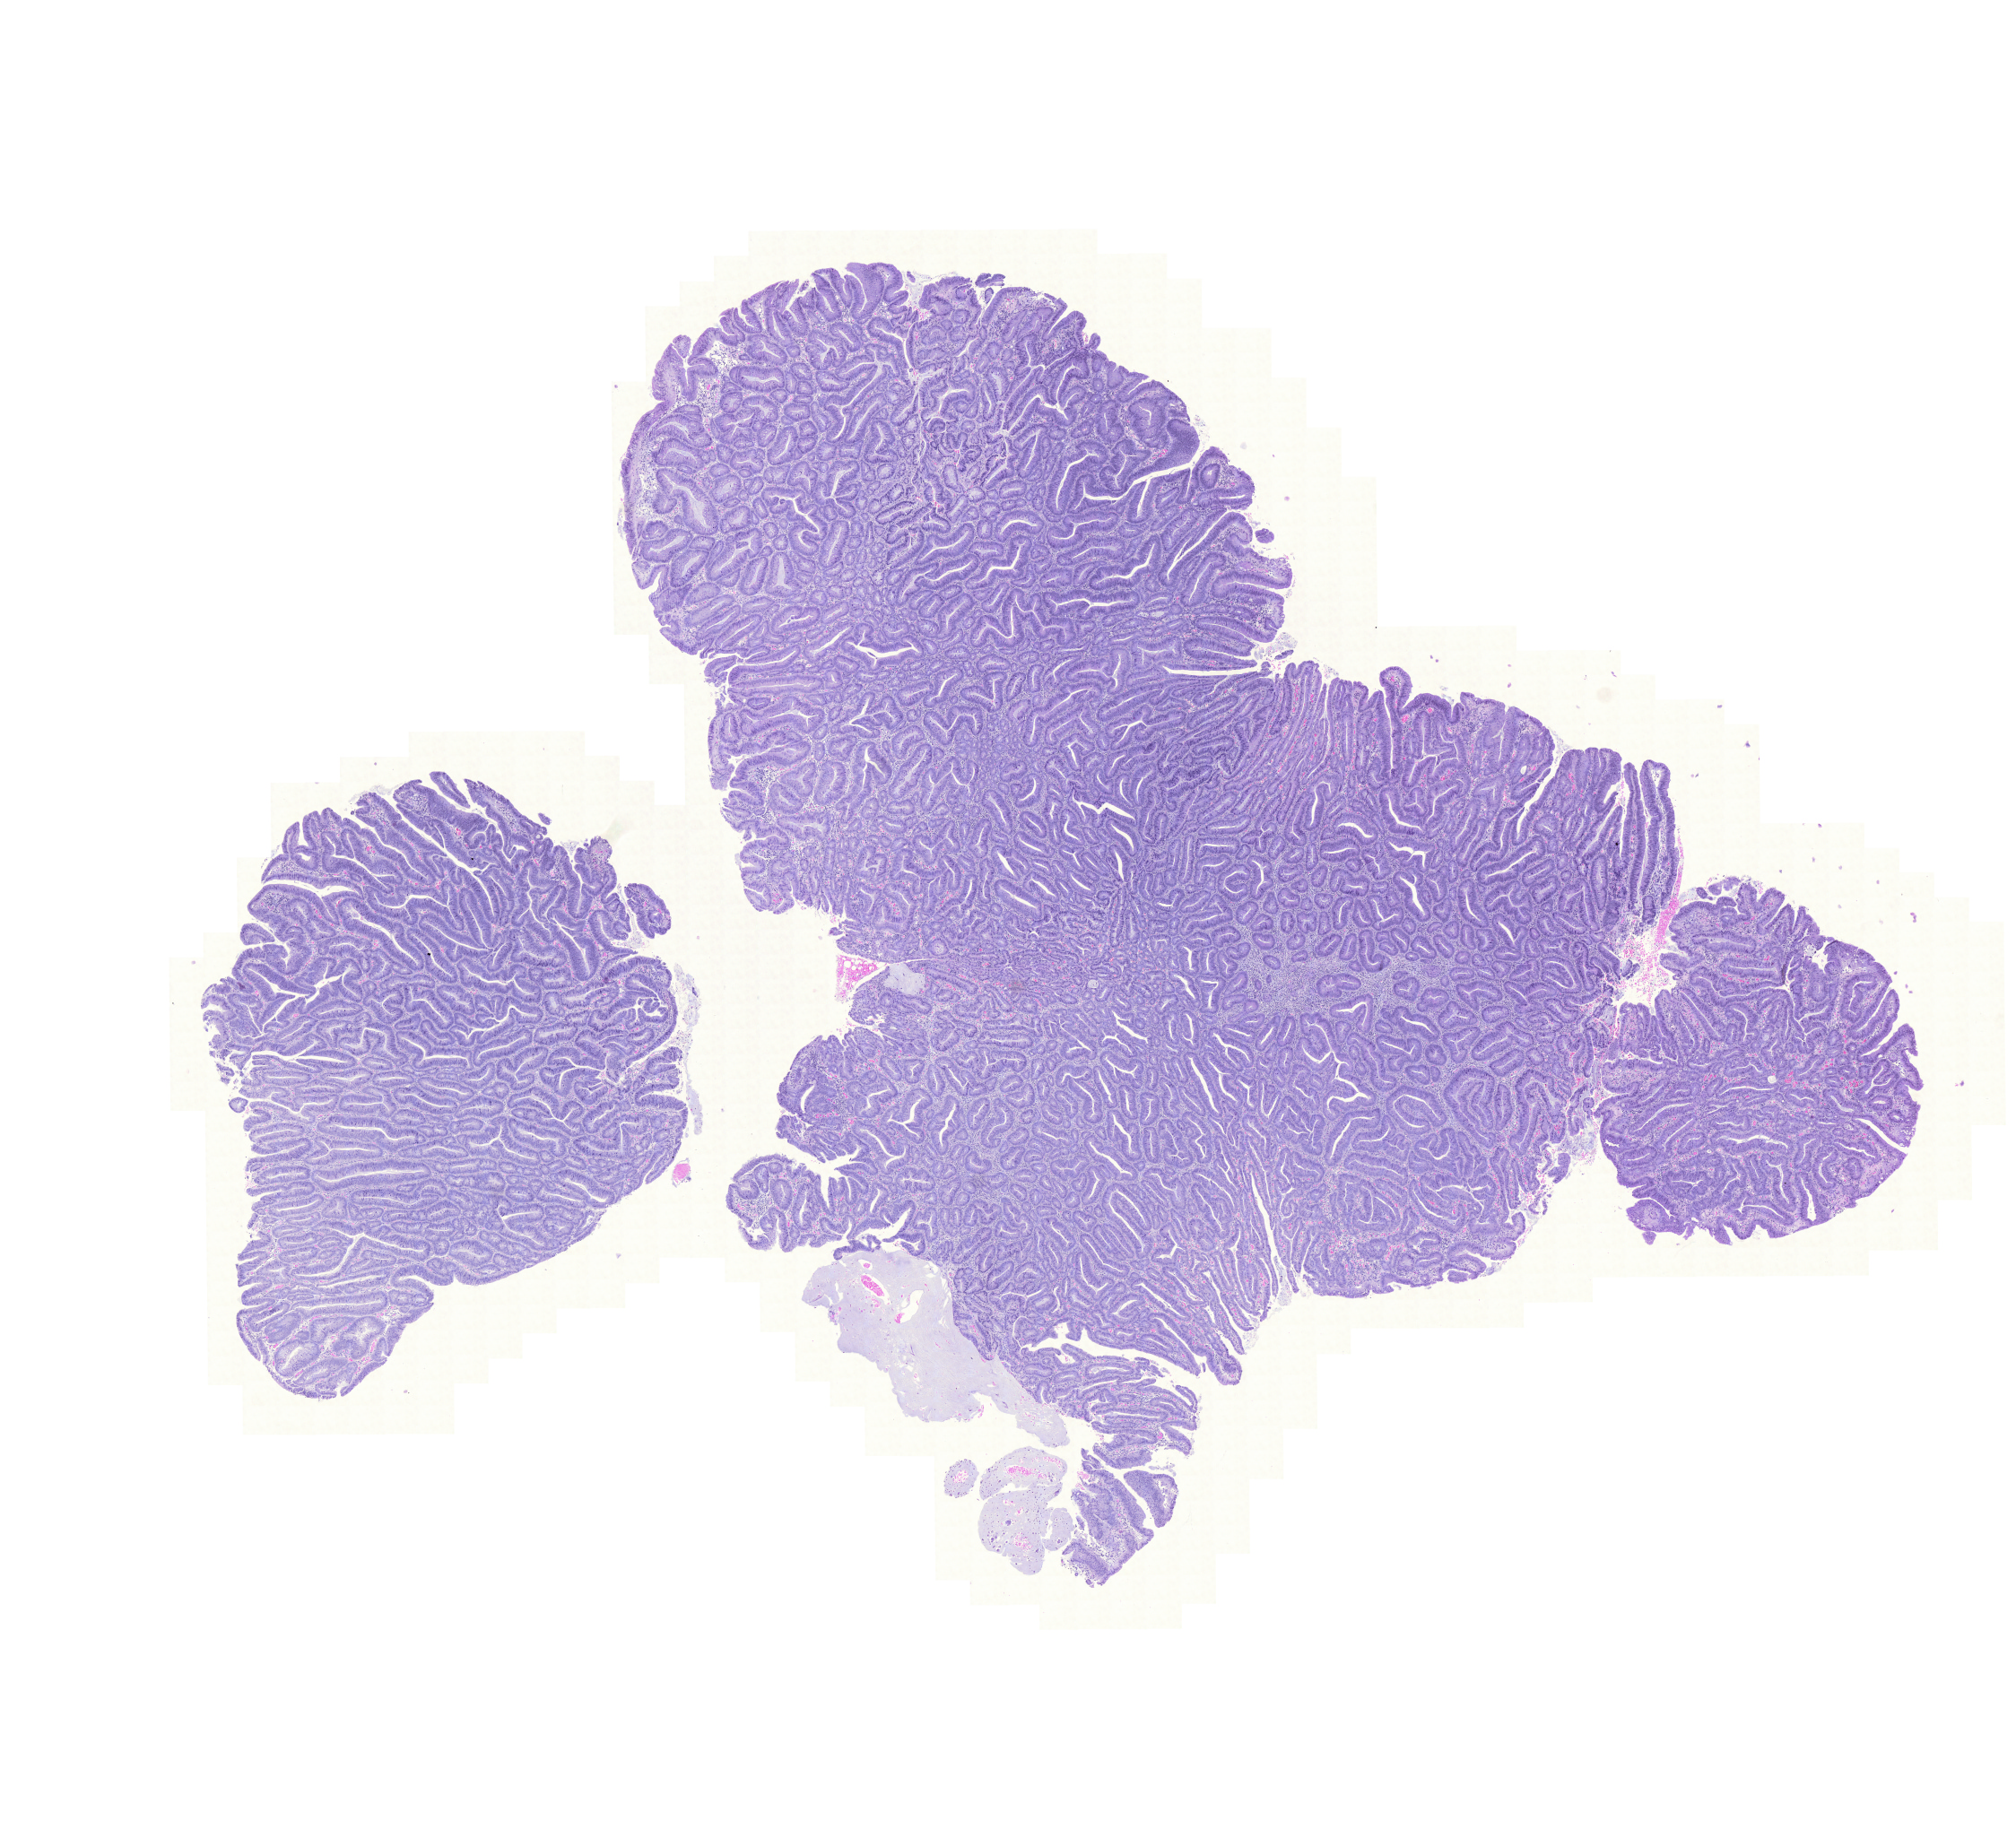
H&E-stained whole-slide image — a low-resolution overview of the entire scanned area, about 16.7 x 15.2 mm; formalin-fixed paraffin-embedded (FFPE) diagnostic section; primary tumour sample from the rectum. Female, age 64 years at initial diagnosis.
Diagnosis: Adenocarcinoma, NOS. Lymph nodes positive (case pathology): 0 of 18 examined. AJCC pathologic stage: I (6th edition).